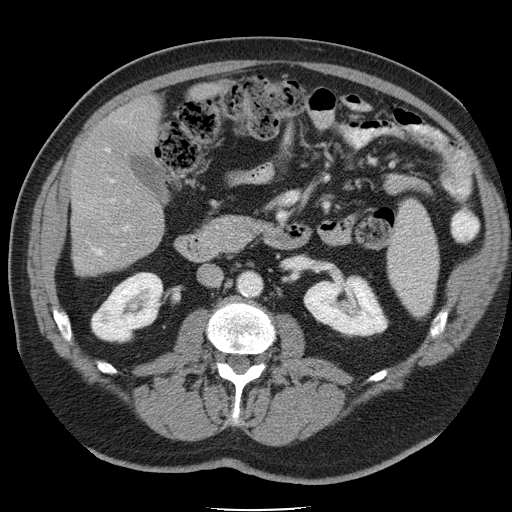
Contrast-enhanced abdominal CT, one axial slice; position 15 of 45 along the scan axis; intravenous contrast given; soft-tissue window (W 400 / L 40 HU); 512 × 512 image matrix, field of view 386 × 386 mm. Male patient, age 65 years. Case-level facts recorded for this patient, not image findings: diagnosis: colorectal cancer liver metastases, imaged before liver resection; multiple liver metastases: yes; largest metastasis: 4.9 cm; disease in both lobes: no.
Structures marked on this image (expert manual segmentation):
- liver: bounding box [x1, y1, x2, y2] px = [72, 100, 164, 275]
- planned liver remnant (the part of the liver to remain after resection): [92, 88, 210, 164]
- portal vein (with intrahepatic branches): [111, 180, 113, 182]